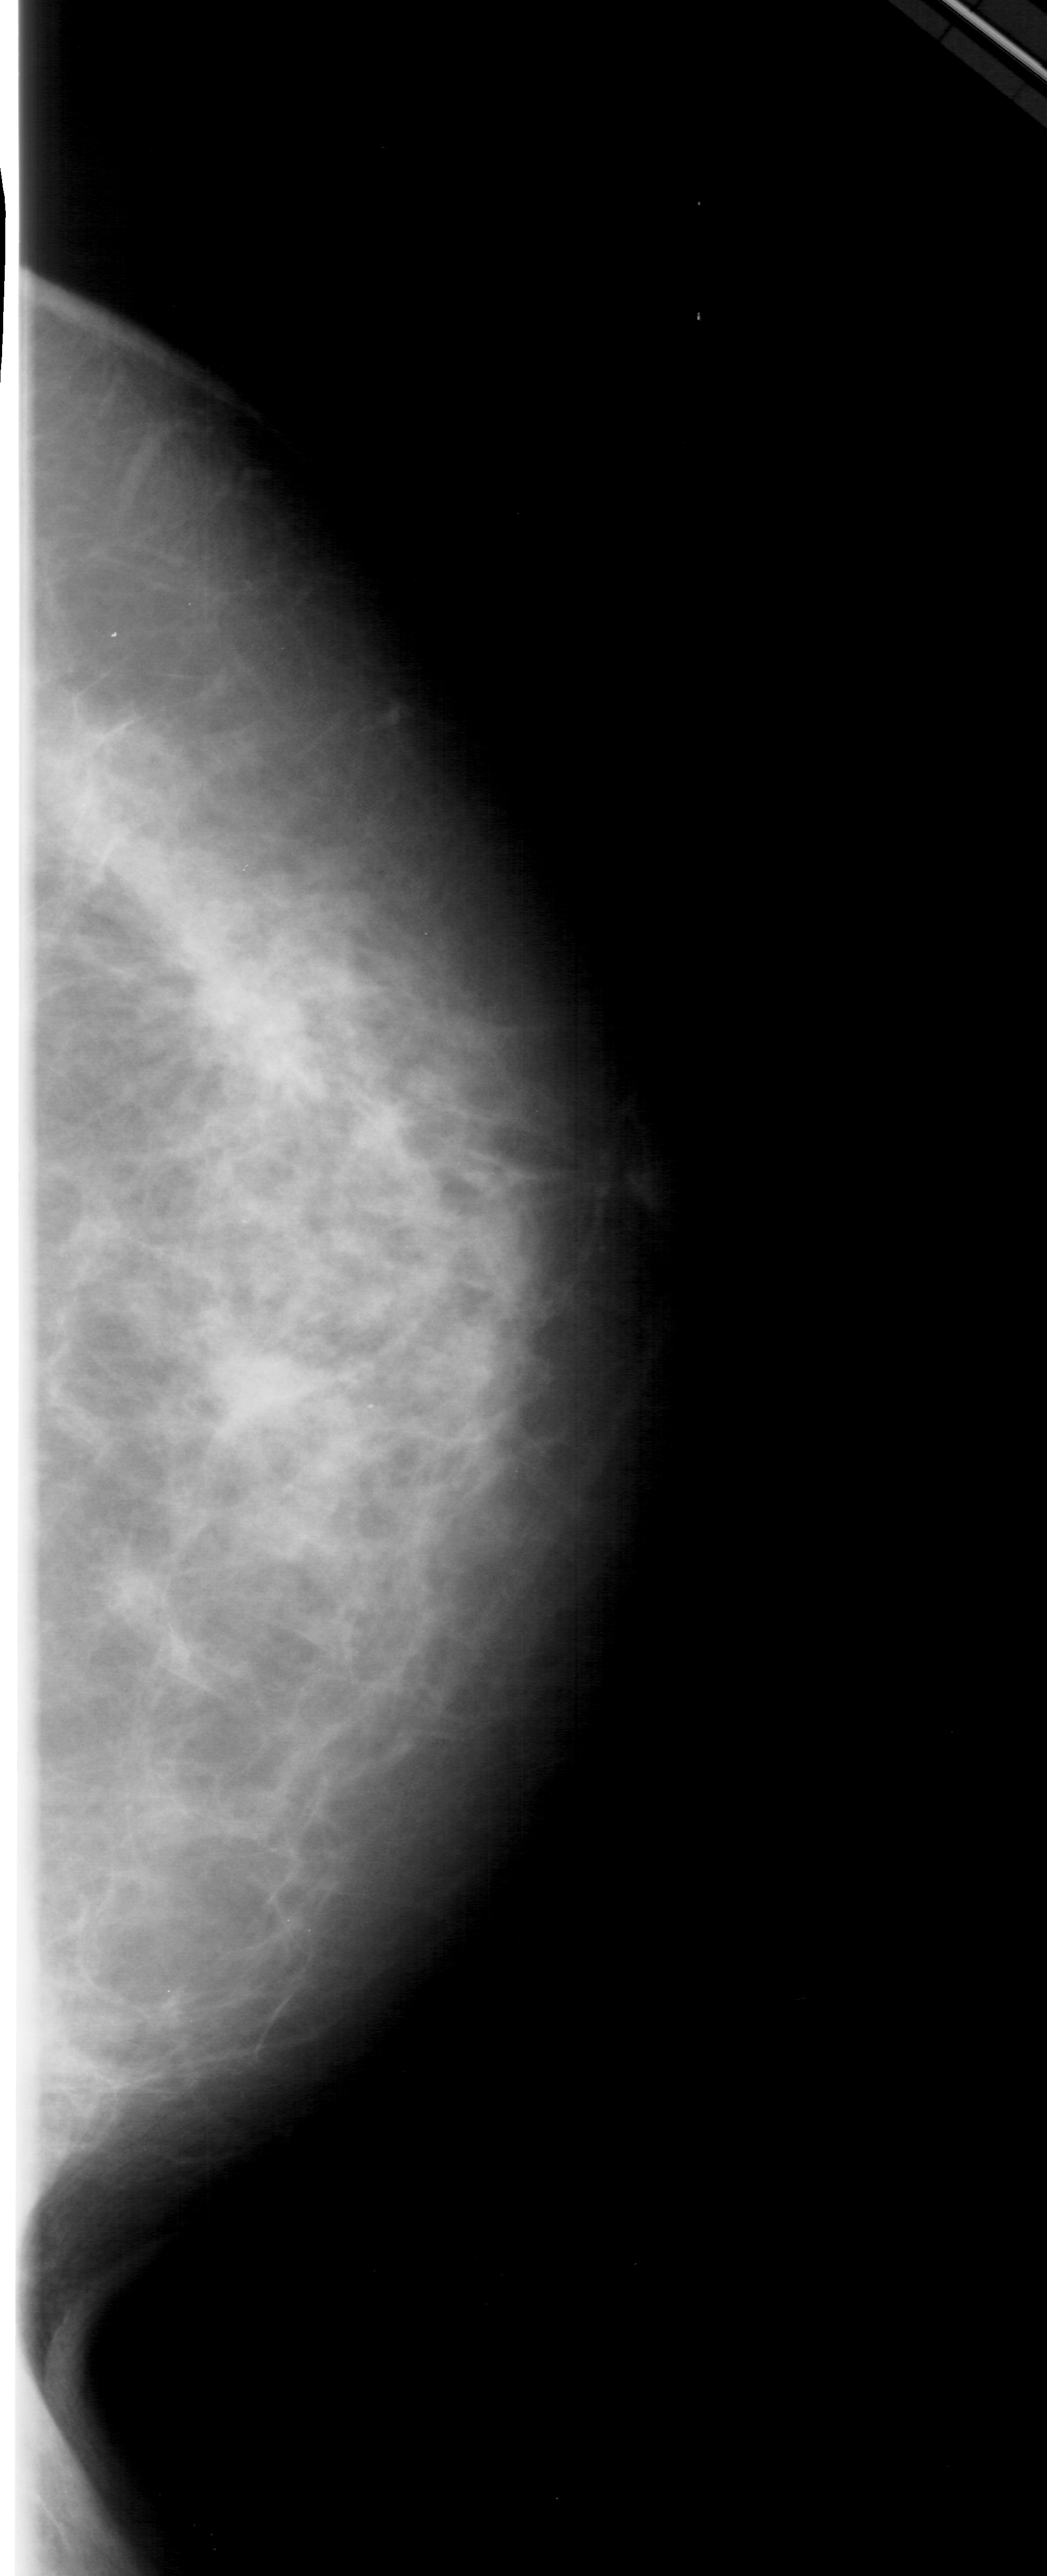
Mammogram (digitized film). Right breast. CC view. Breast composition: extremely dense (BI-RADS density category 4 of 4). 1047 × 2576 image matrix.
Expert-marked regions of interest on this image (one box per marked abnormality):
- mass, shape architectural distortion, margins ill defined; BI-RADS assessment category 4; subtlety rating 1 on a 1 (subtle) to 5 (obvious) scale; pathology result (as recorded, not read from the image): benign: bounding box (x1, y1, x2, y2) in pixels: (107, 875, 381, 1130)